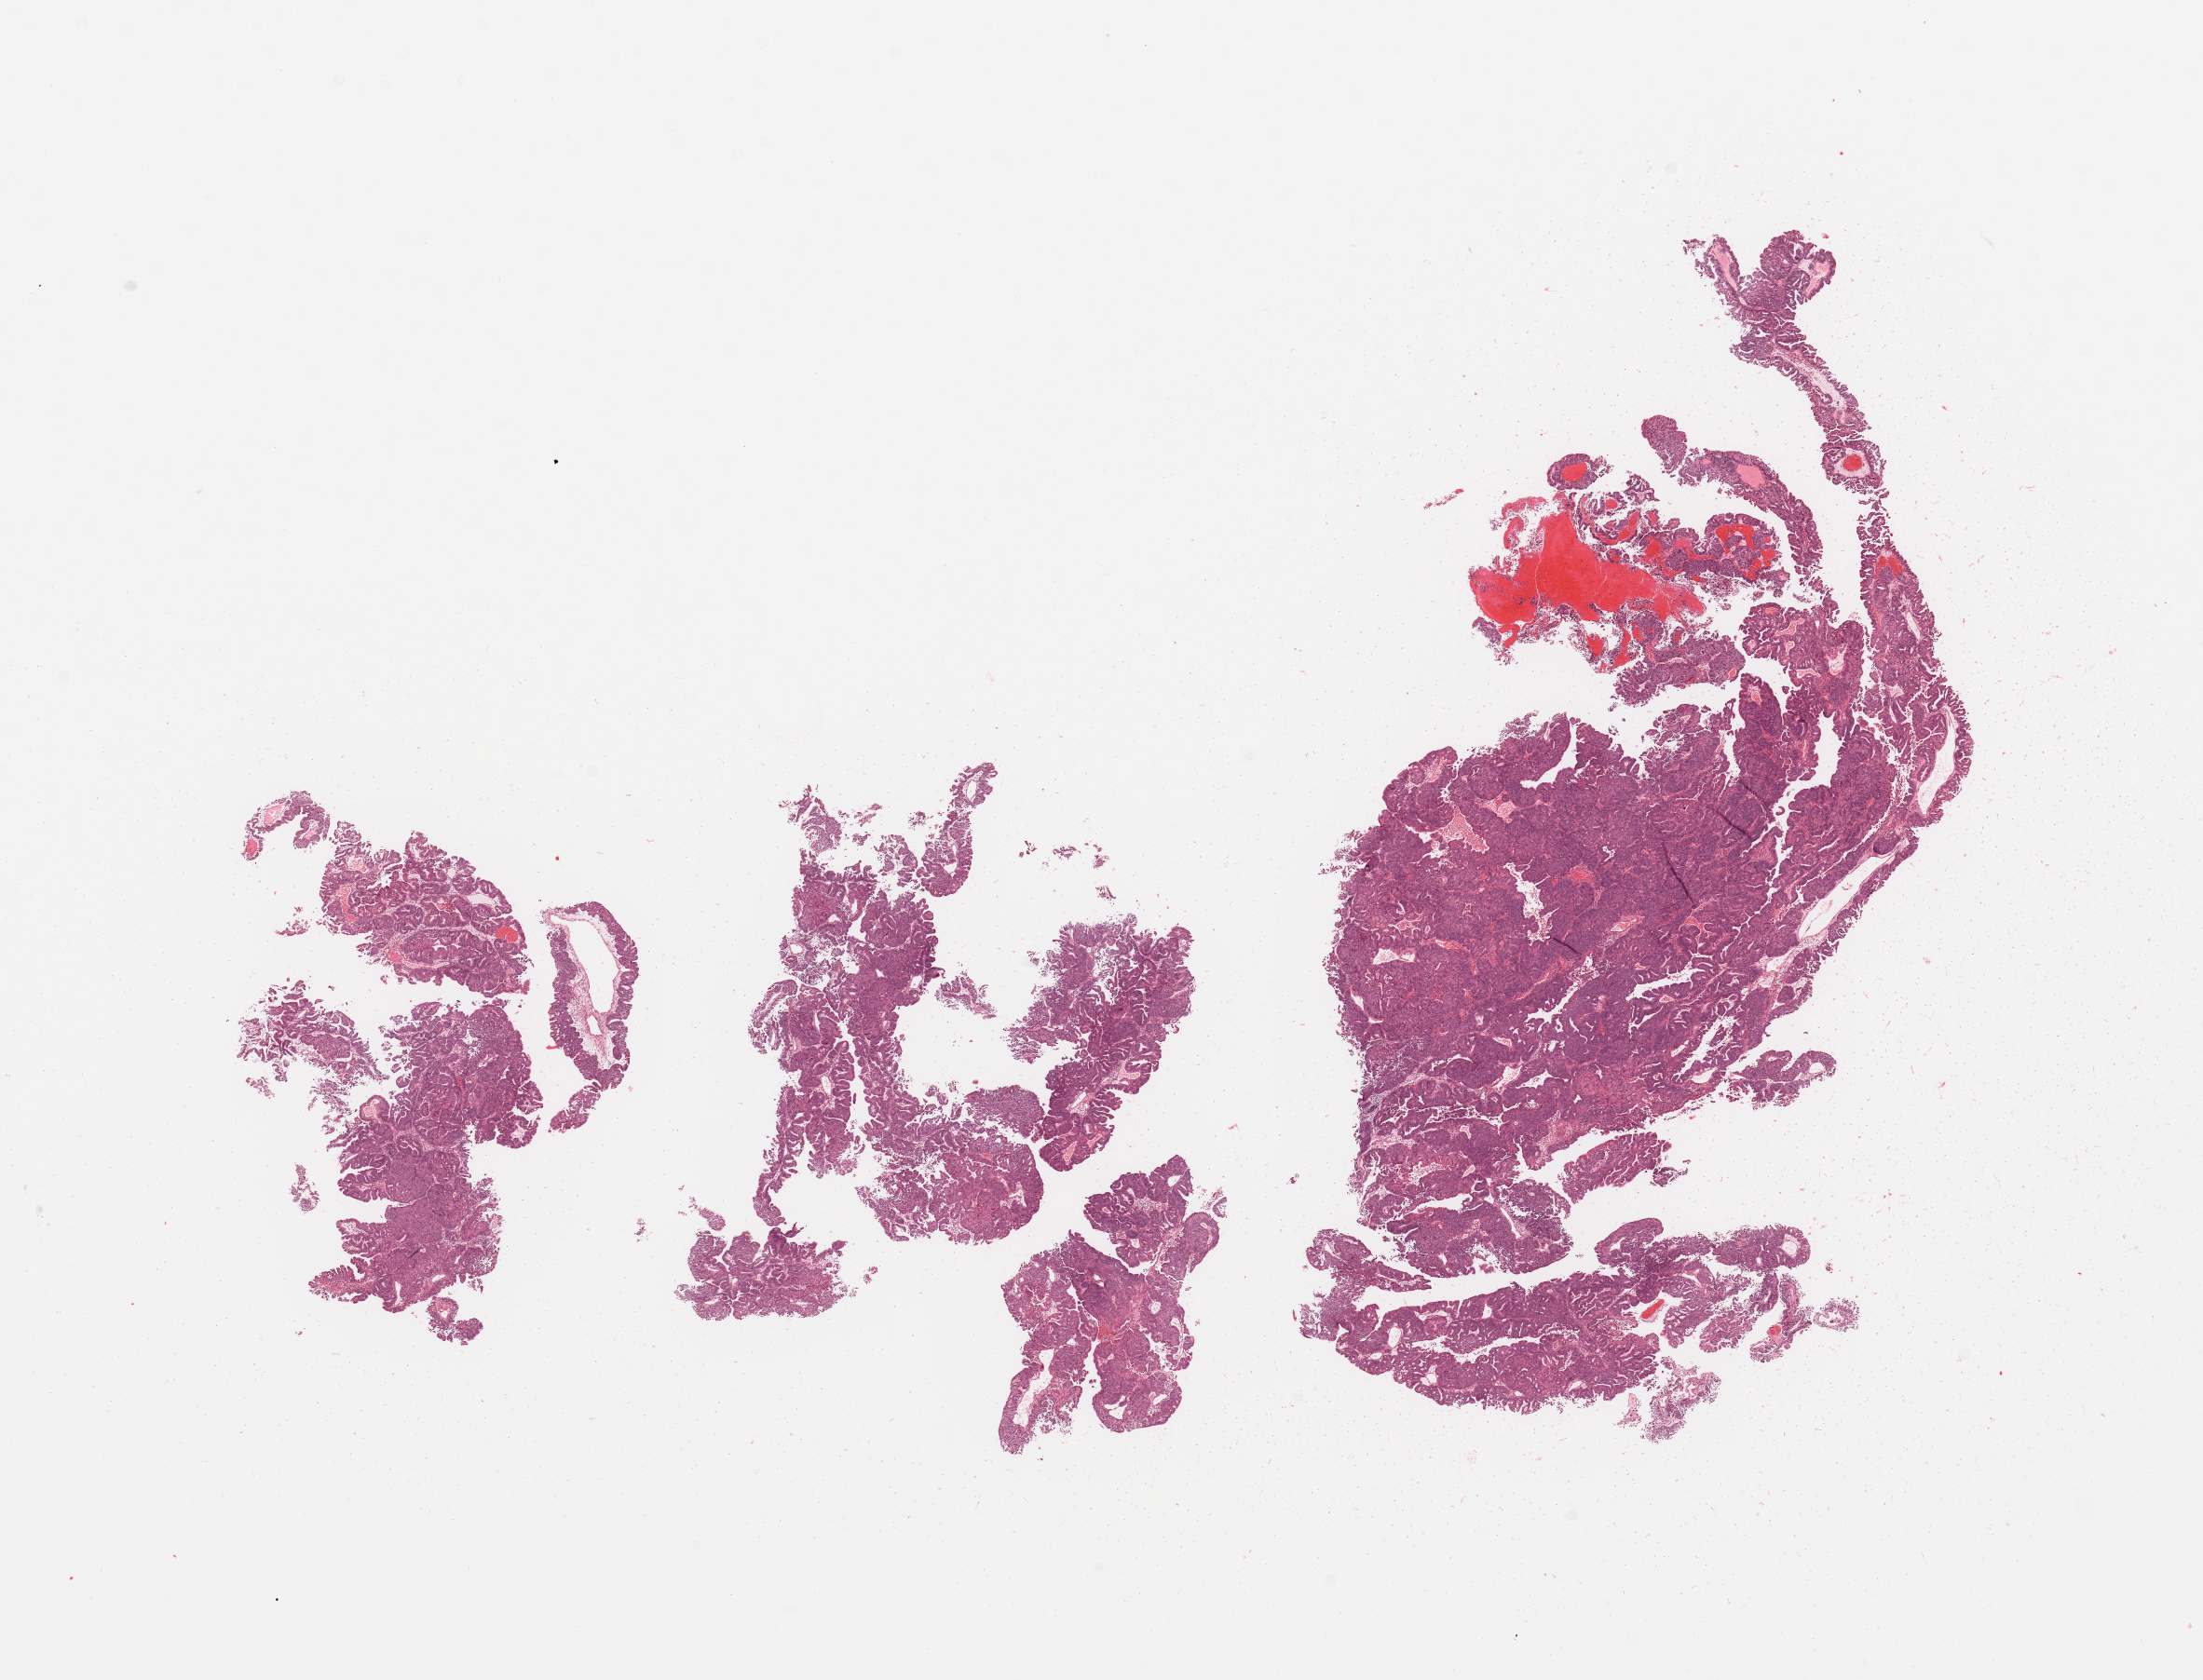
Digitized Hematoxylin and eosin (H&E) stained tissue section (whole slide), shown as a low-resolution overview of the whole scanned area (about 18.7 x 14.3 mm, slide scanned at 20x). Tumour tissue sample, uterus. 81-year-old female patient. Histologic grade: G2 (moderately differentiated).
AJCC pathologic stage: I. Diagnosis: Endometrioid adenocarcinoma, NOS.